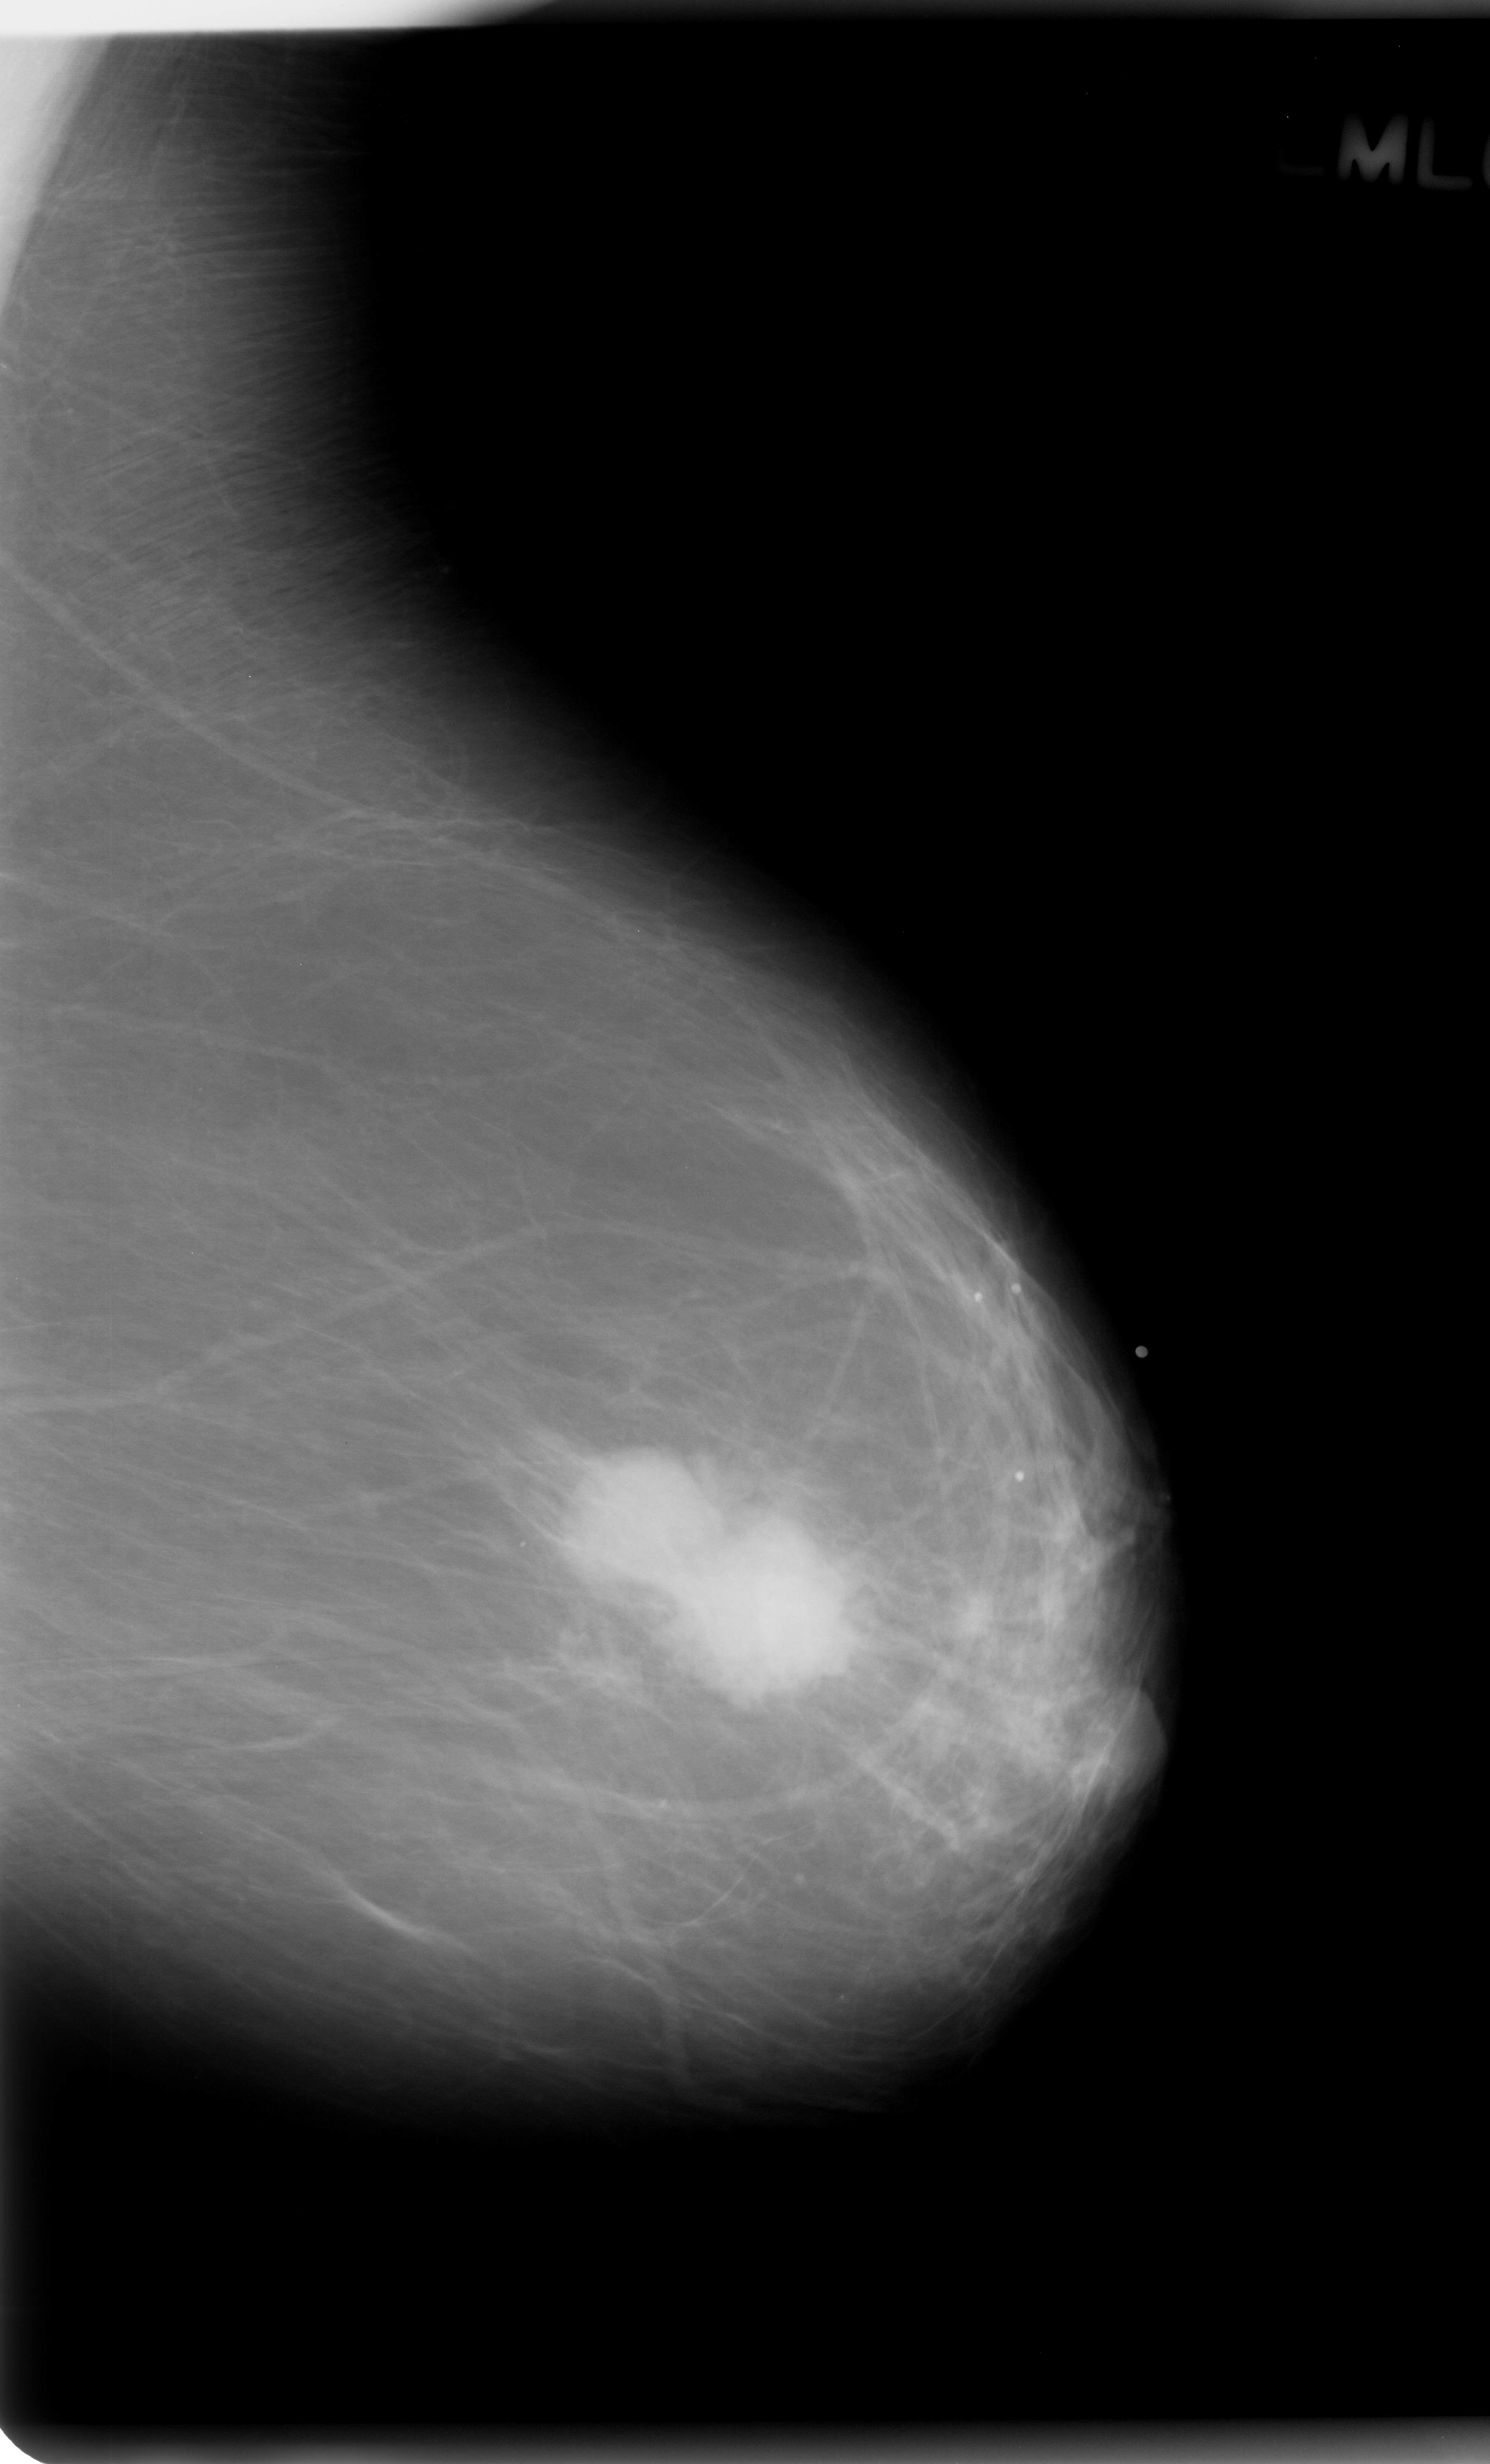
Mammogram (digitized film); left breast; mediolateral oblique (MLO) view; BI-RADS breast density category 1 (scale 1–4); 1490 × 2464 image matrix.
Expert-marked regions of interest on this film, with their recorded descriptors:
- mass, shape lobulated, margins microlobulated; BI-RADS assessment category 5; pathology (as recorded): malignant: bounding box <656,1502,880,1708> (left, top, right, bottom; pixels)